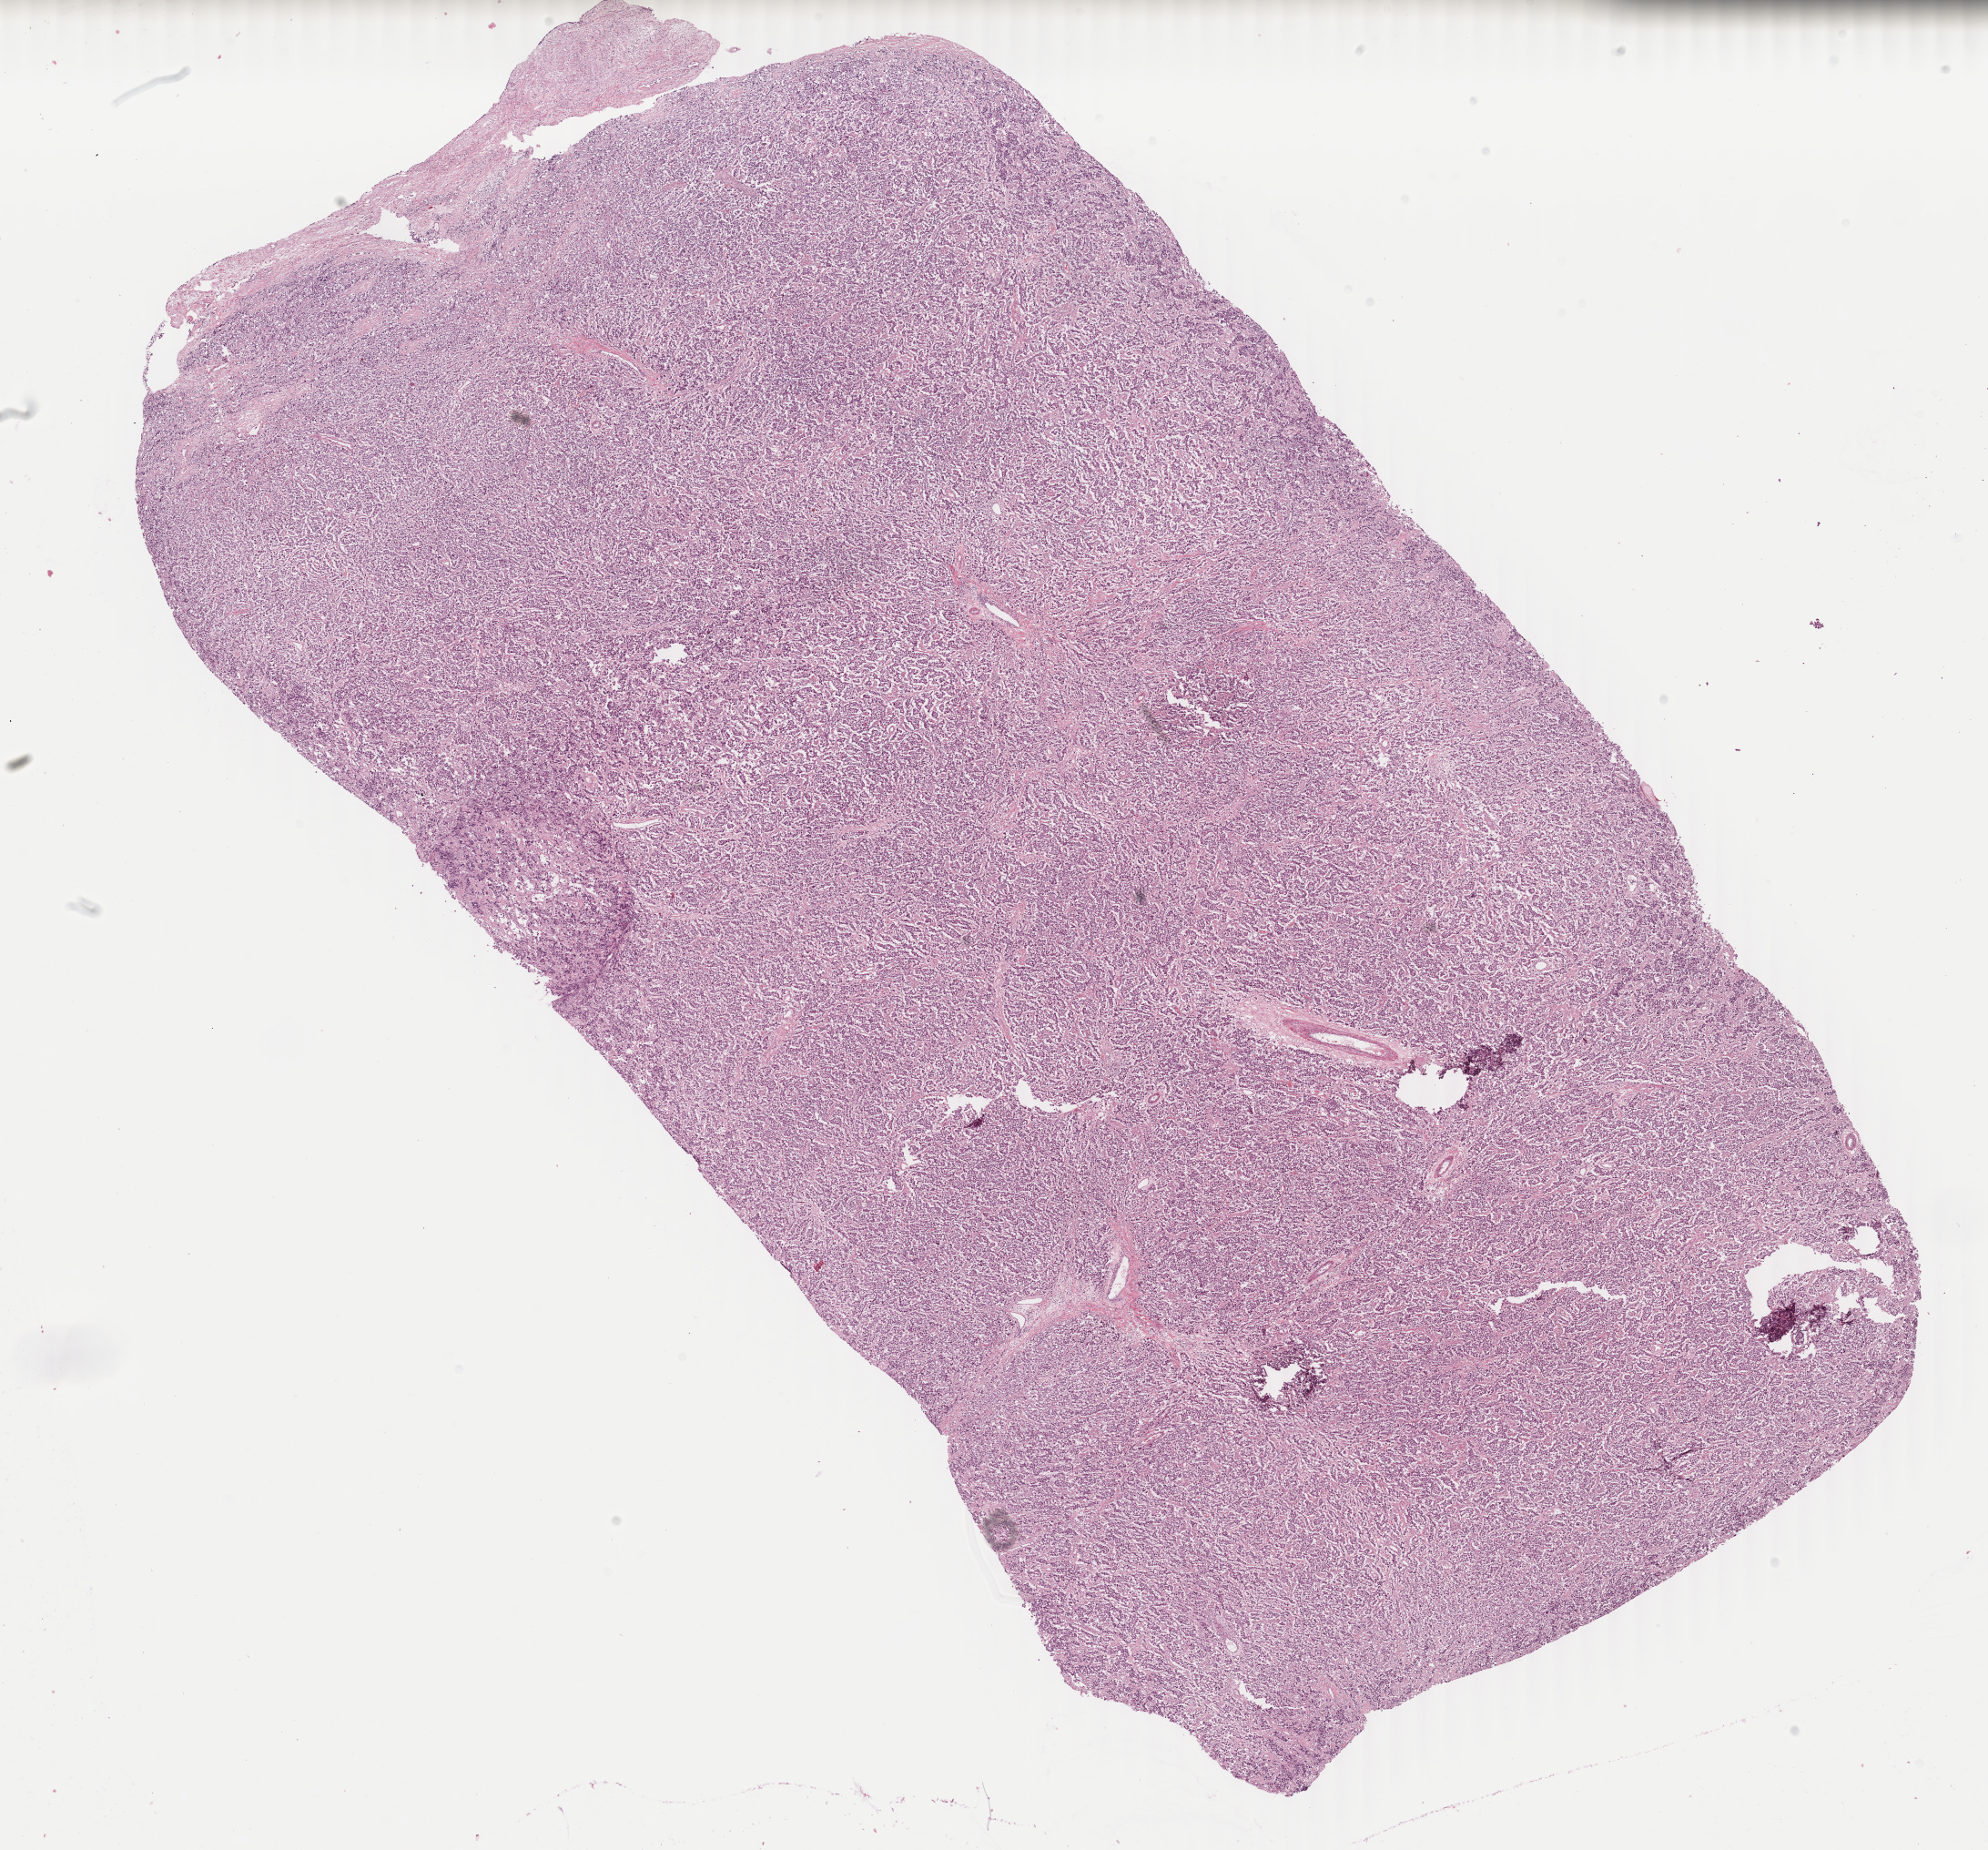
Hematoxylin and eosin (H&E) stained whole-slide image — low-resolution overview of the scanned area, about 17.4 x 16.2 mm, formalin-fixed paraffin-embedded (FFPE) diagnostic section, sample: primary tumour, testis. Patient: male, age at initial diagnosis 34 years.
Histologic diagnosis: Seminoma, NOS.